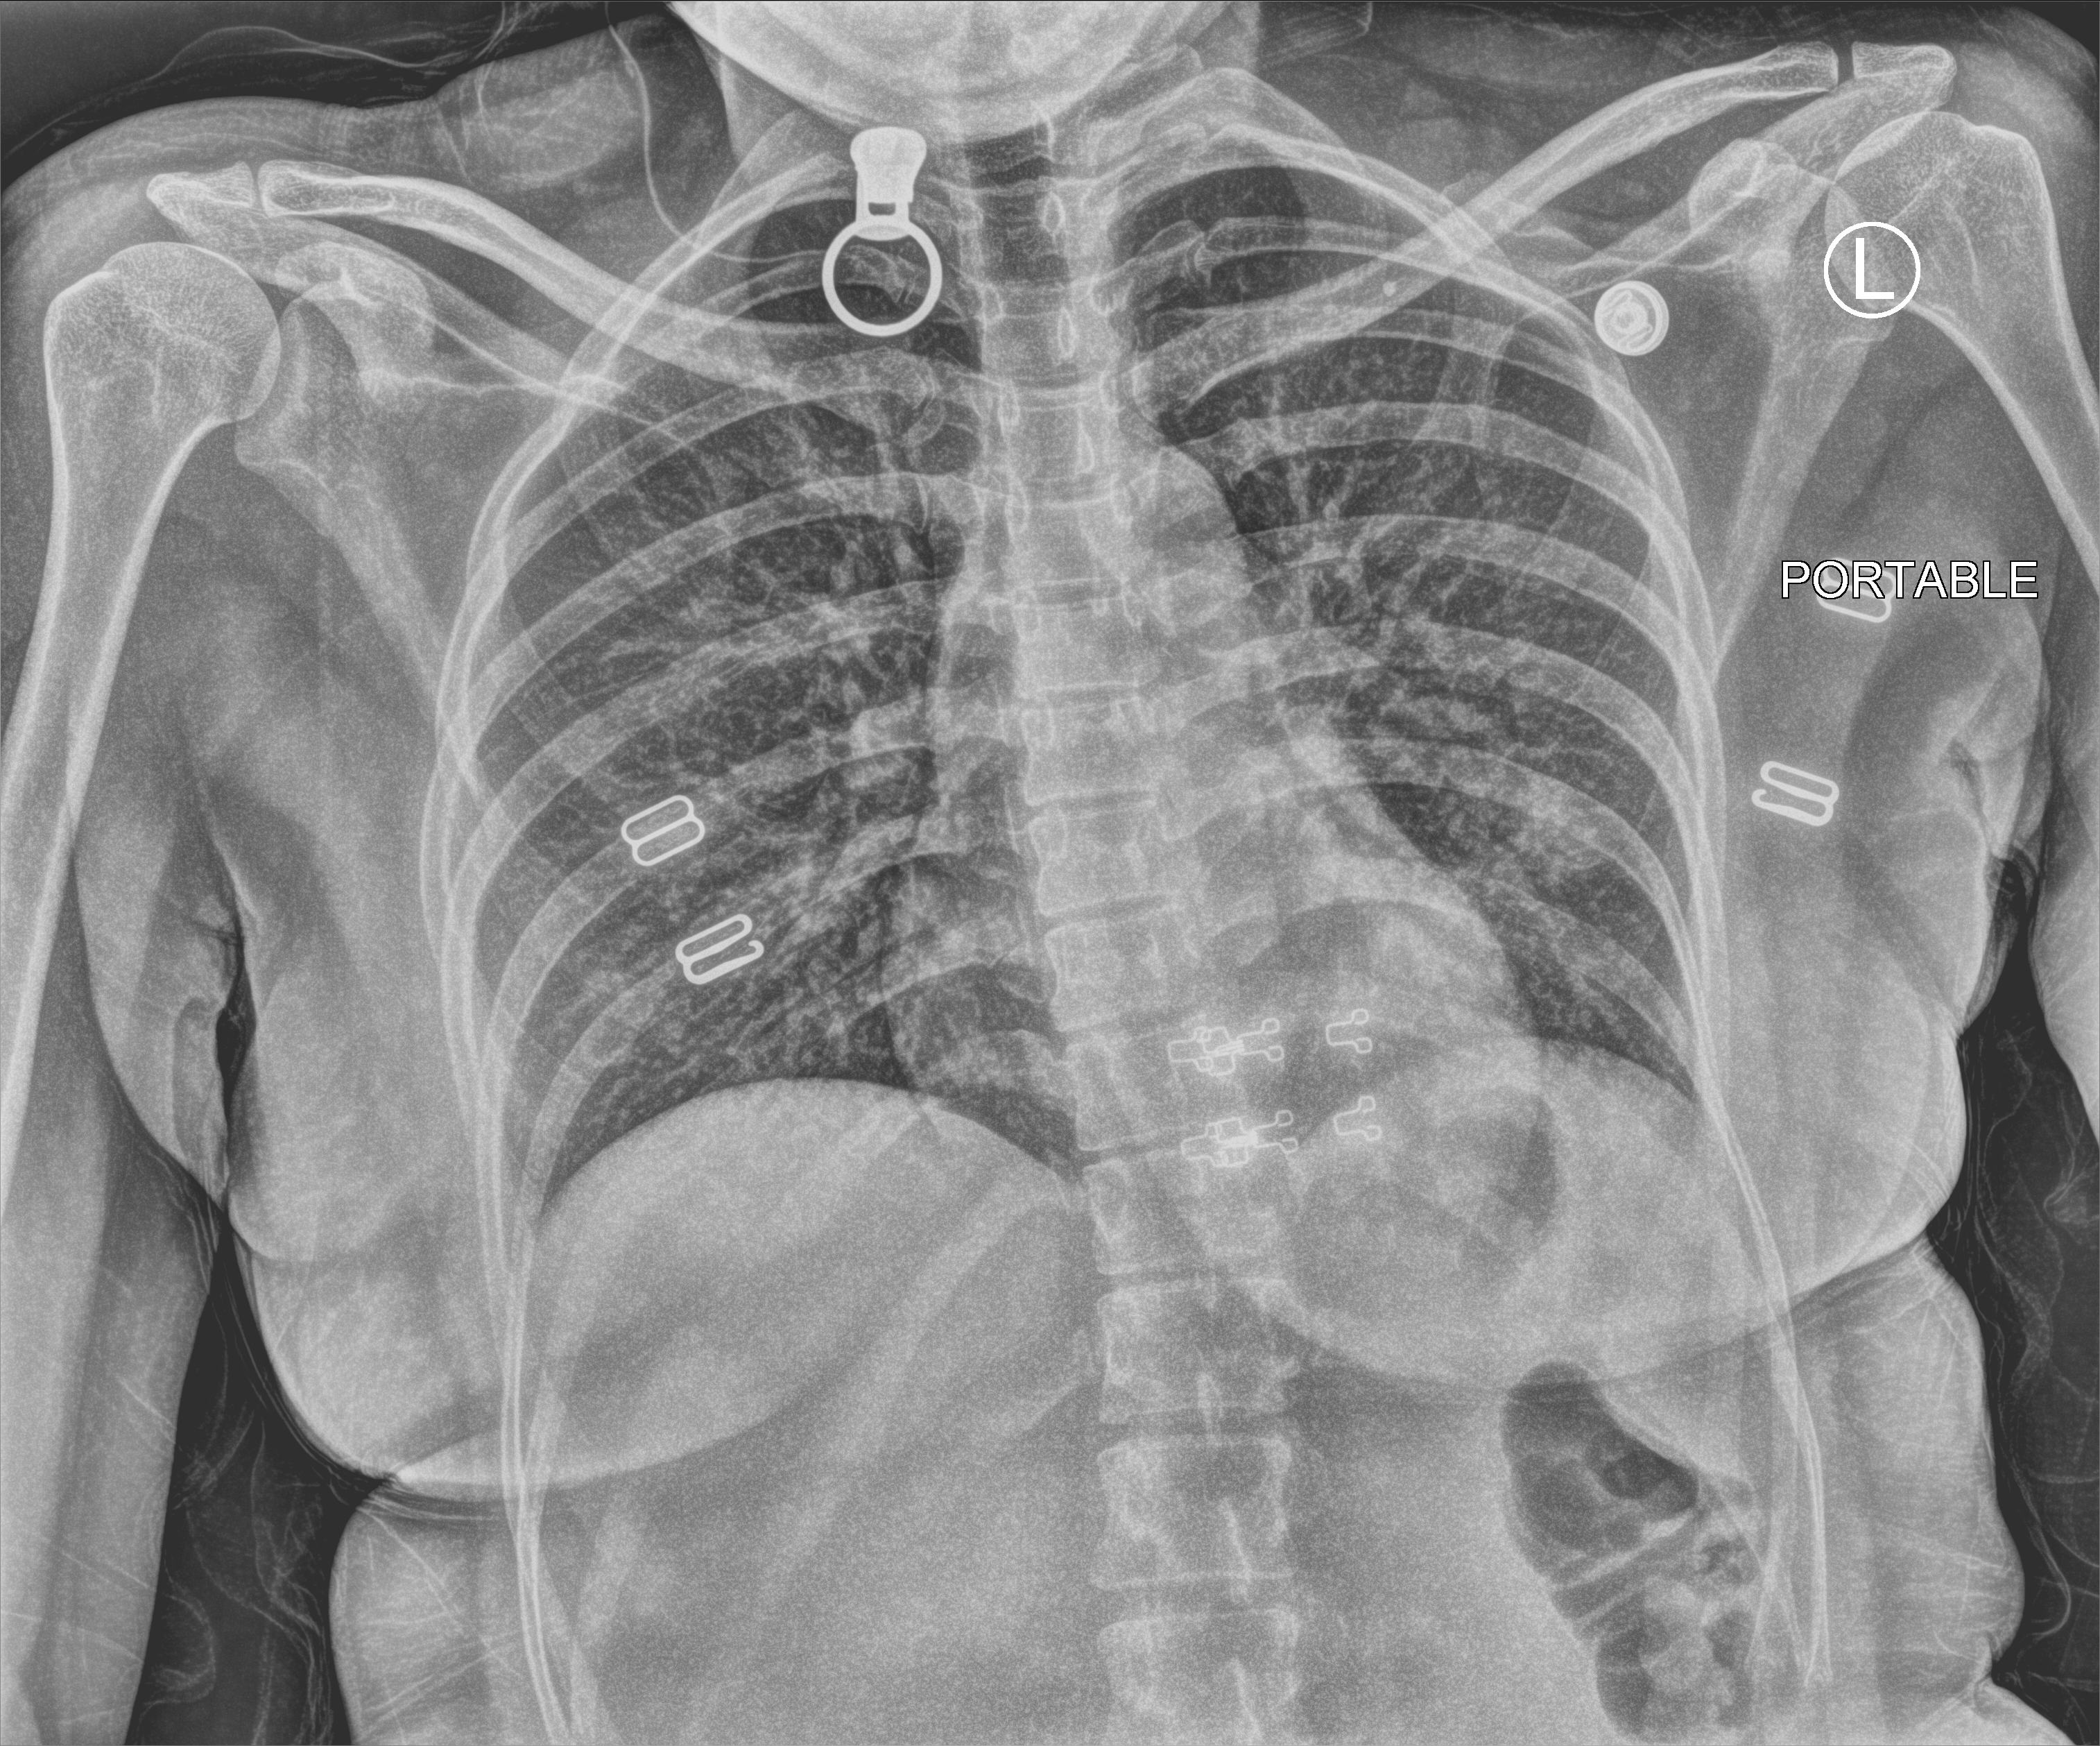
Bedside chest radiograph (computed radiography). Female patient hospitalised with COVID-19, age 18–59 years.
Admission-level facts for this patient (not findings on this image; timing relative to this image not recorded):
- admitted to intensive care during this hospital stay: no
- mechanically ventilated during this hospital stay: no